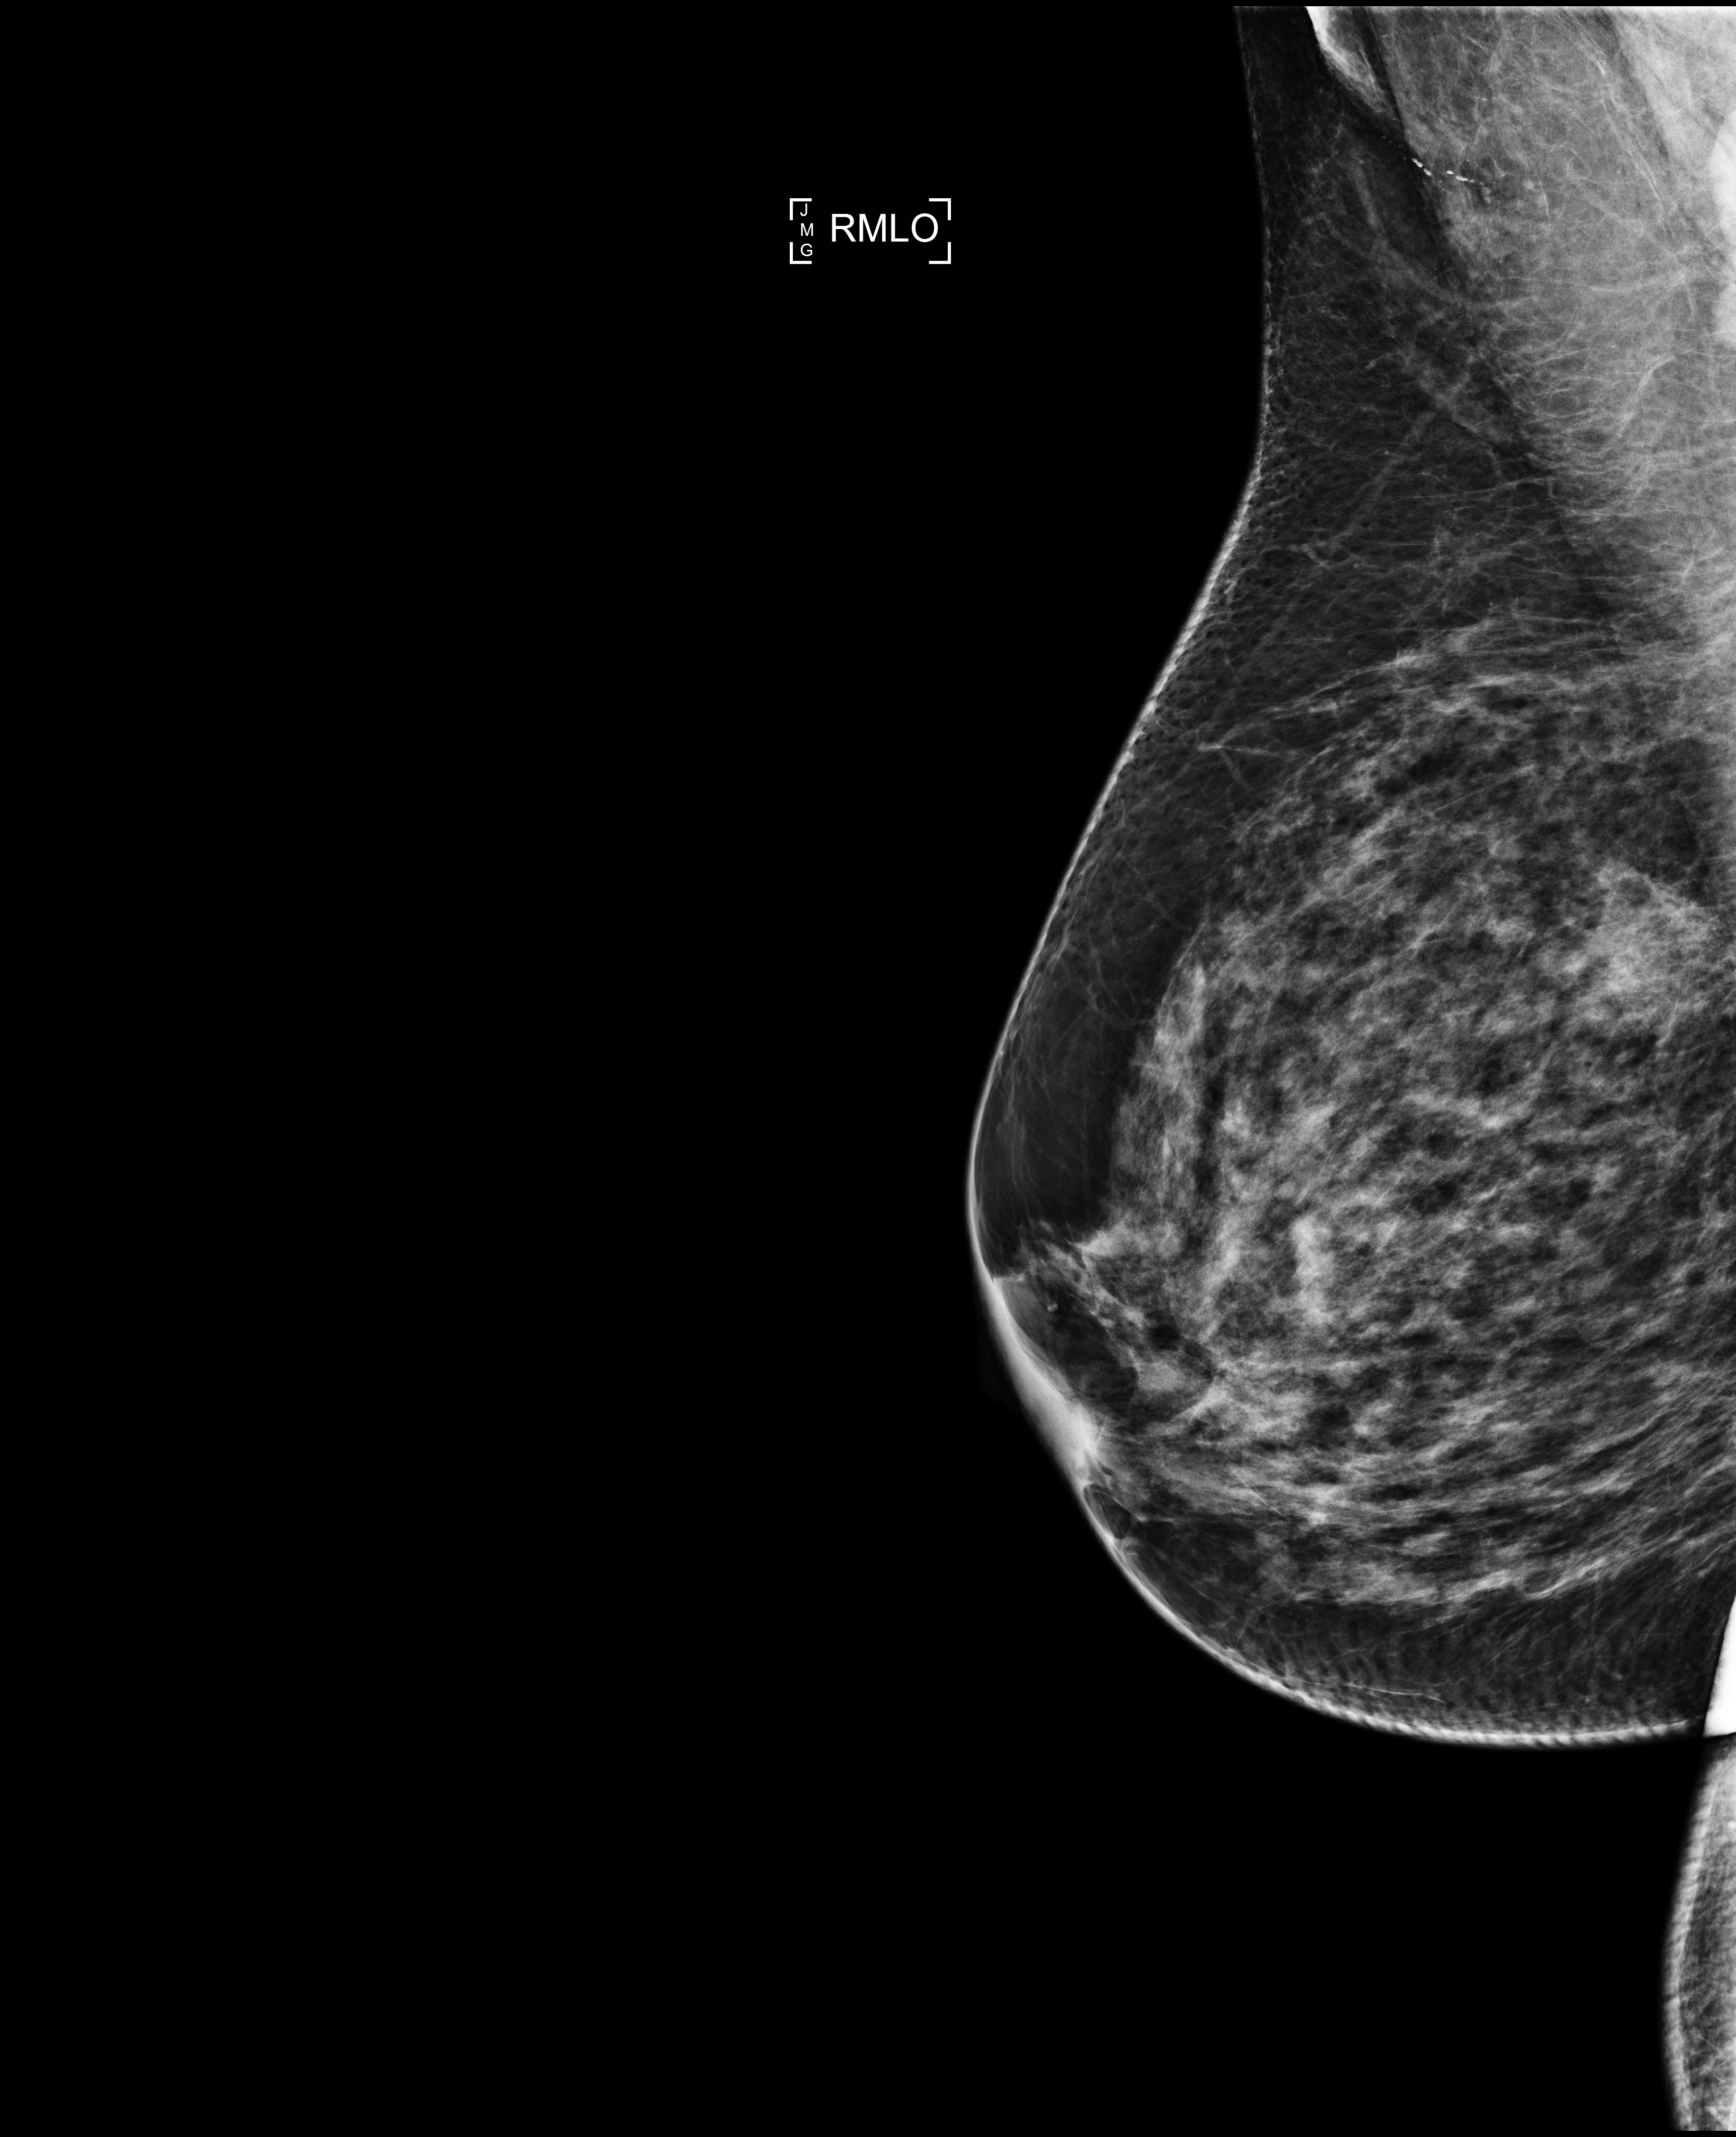
Annual screening mammography examination, compressed breast thickness 73 mm, system: Selenia Dimensions. Patient aged 55 years (female).
Image type: full-field digital mammogram. Breast: right. Projection: medio-lateral oblique projection. BI-RADS breast density category at the screening exam (both breasts, scale 1–4): 3. Final BI-RADS category for the screening round (tomosynthesis exam, both breasts): category 1. Recall: no recall after this screen.